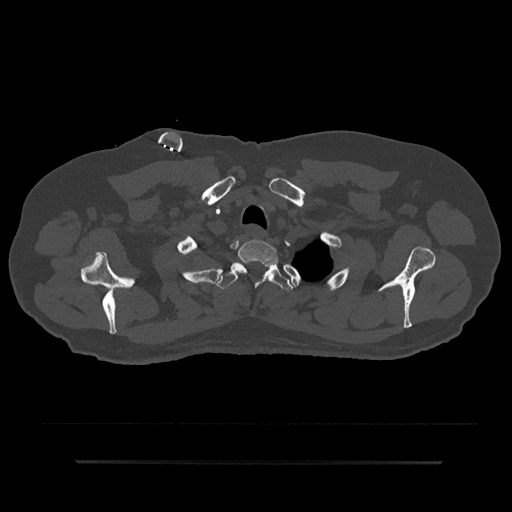
CT including the spine, one axial slice; reconstruction kernel Br40s/3; bone window (W 1800 / L 400 HU); 0.5 mm slice thickness; 512 × 512 image matrix. Male patient, age 59 years. From the clinical record (not read from this slice): primary cancer: bile ducts; vertebrae with lytic lesions (as recorded): T10.
Annotated regions visible in this slice (semi-automatically segmented with operator editing):
- T1 vertebra: bounding box <231,239,279,276> (left, top, right, bottom; pixels)
- T2 vertebra: <216,263,293,291>